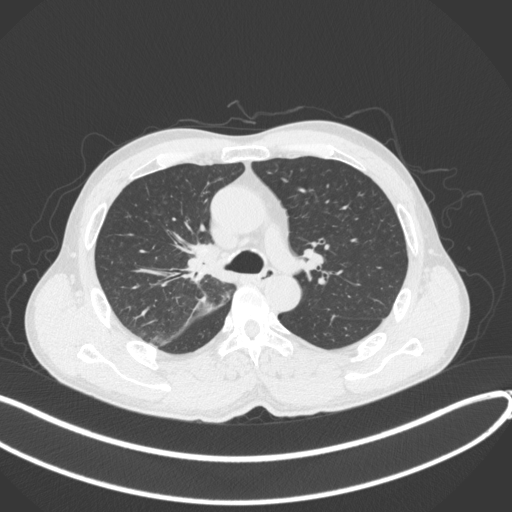
Chest CT, one axial slice; 120 kVp; lung window (W 1500 / L -600 HU); 512 × 512 image matrix, field of view 400 × 400 mm. Male patient, age 53 years. Case-level facts recorded for this patient, not image findings: clinical TNM (as recorded): T1b N0 M0.
Annotated regions visible in this slice (rectangle marked by the reading radiologist):
- lung tumour (recorded histology: squamous cell carcinoma): bounding box <181,236,223,280> (left, top, right, bottom; pixels)